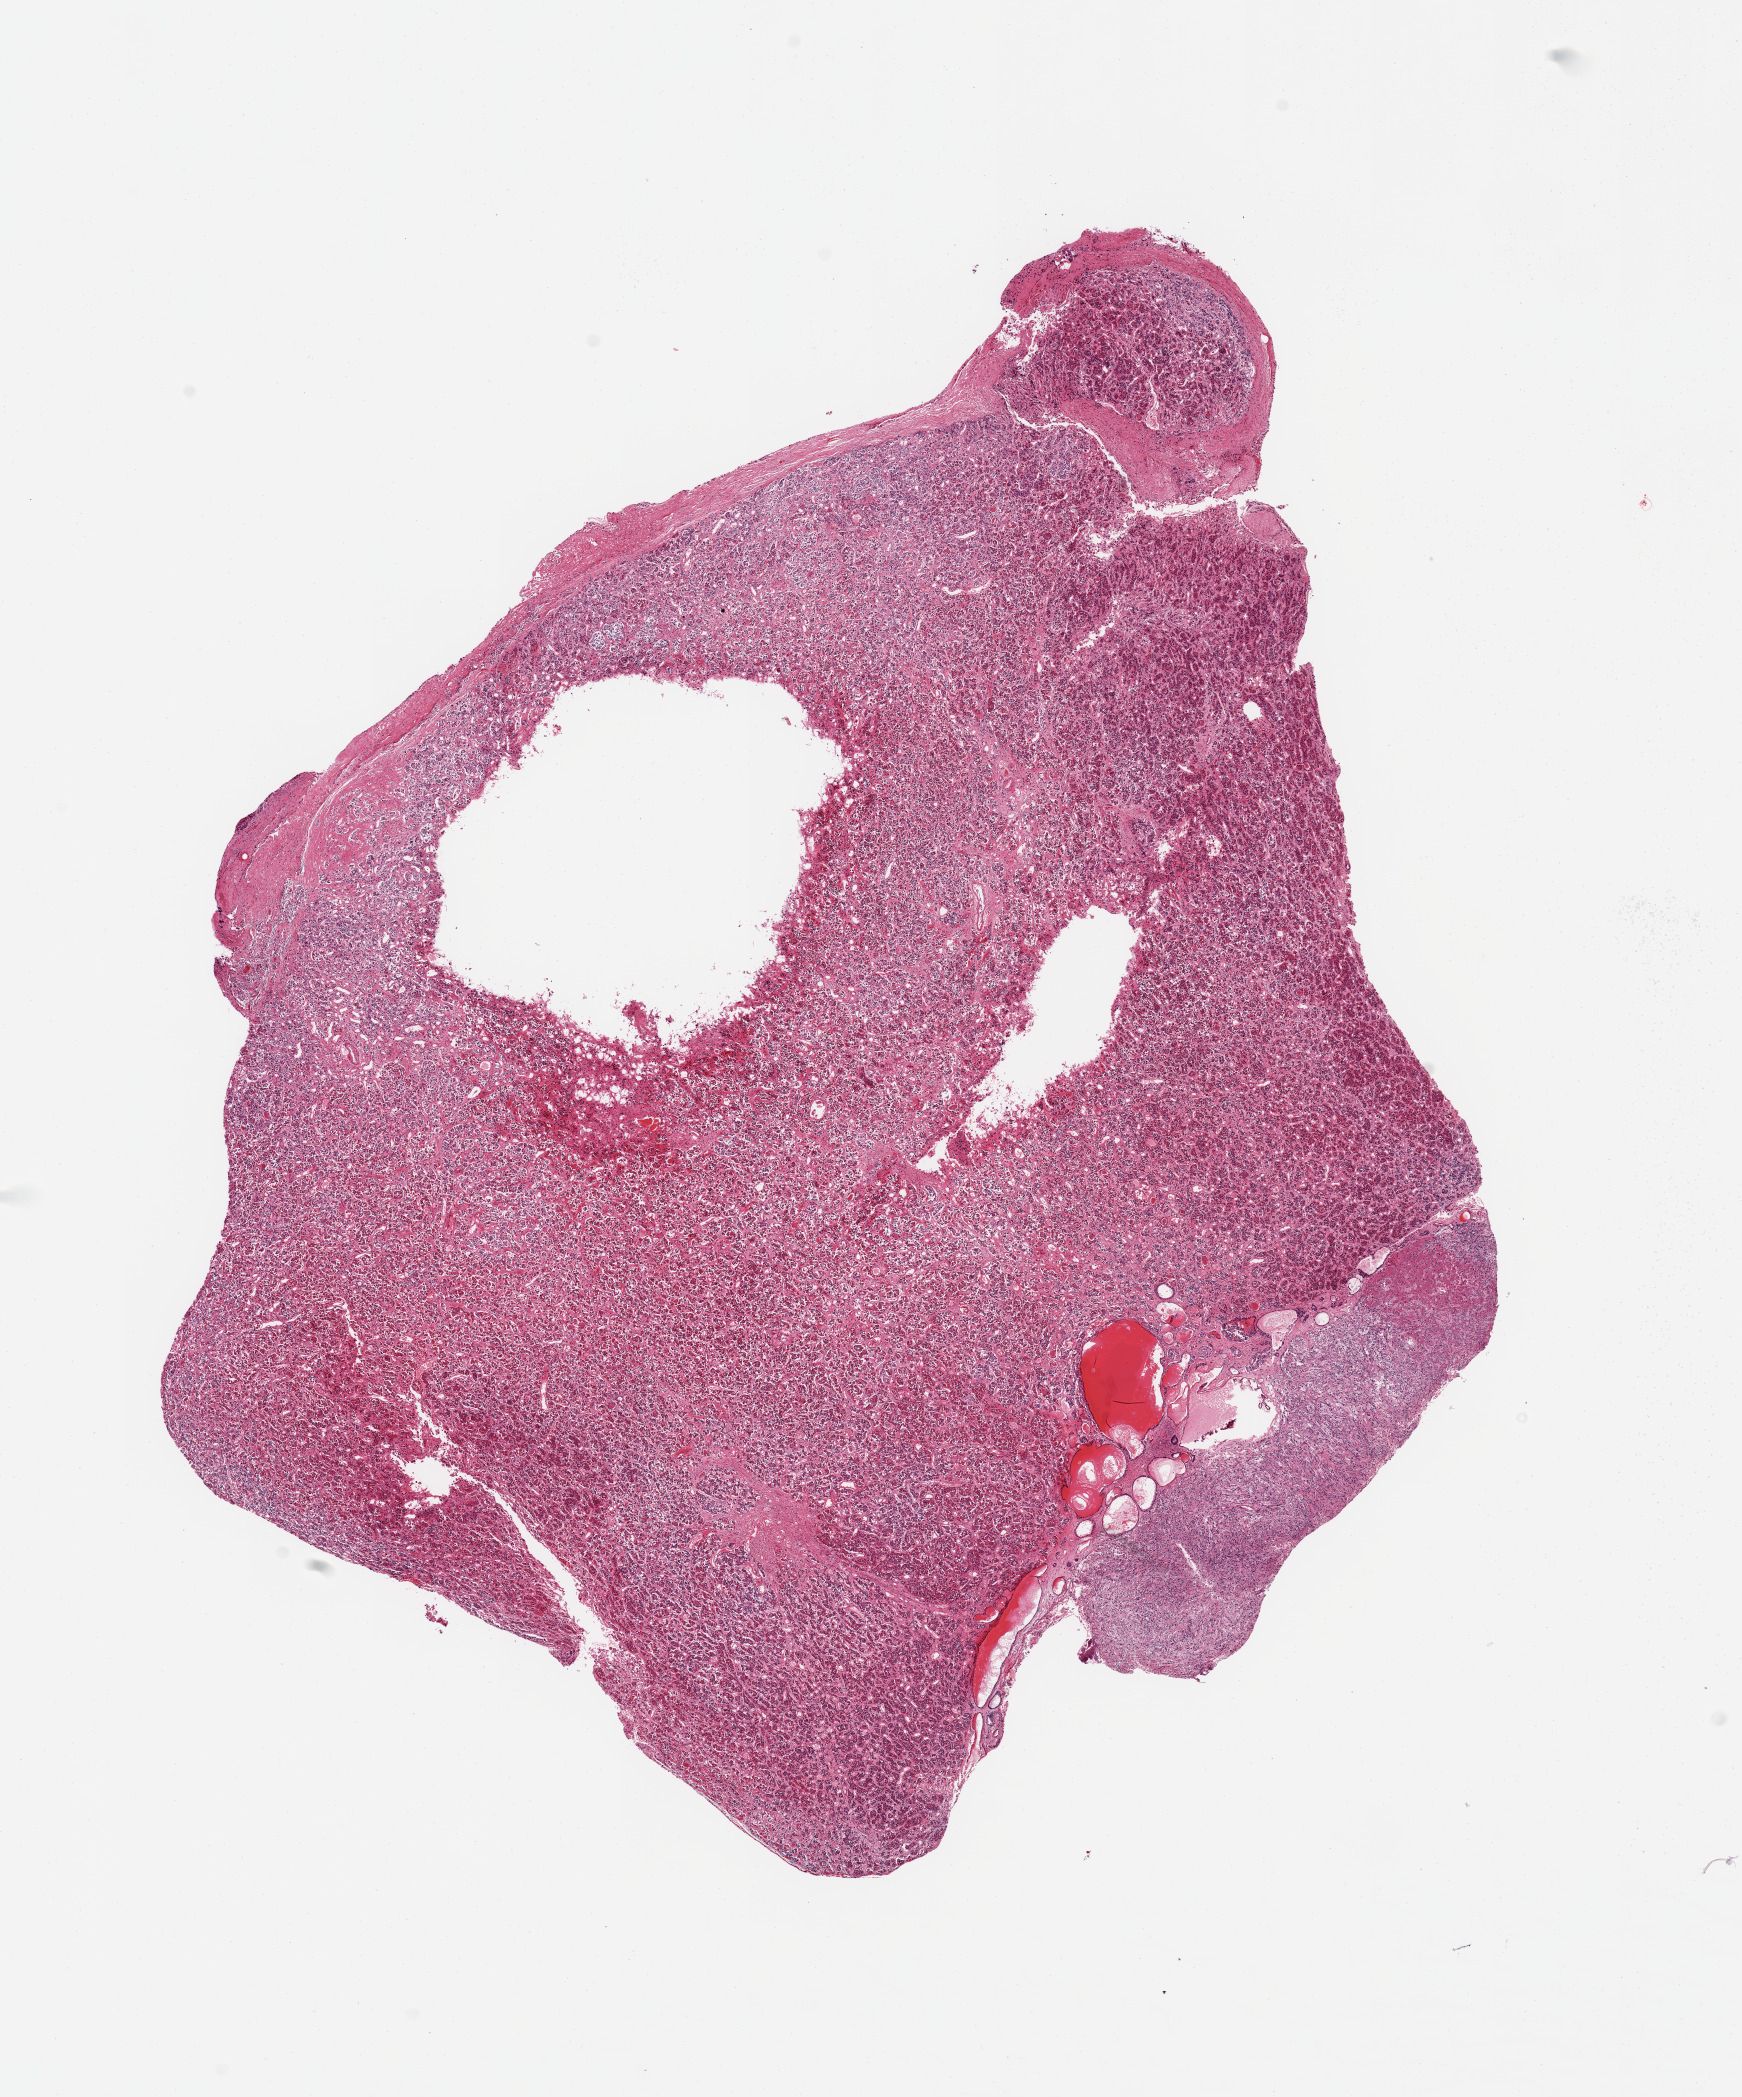
Haematoxylin and eosin whole-slide image, brightfield, shown as a low-resolution overview of the whole scanned area (about 13.8 x 16.6 mm). PAXgene-fixed, paraffin-embedded tissue. Target tissue: pituitary. Donor tissue sample. Donor: female.
Review note (as recorded): 1 piece mainly adenohypophysis; ~3.5x1mm nubbin of neurohypophysis.